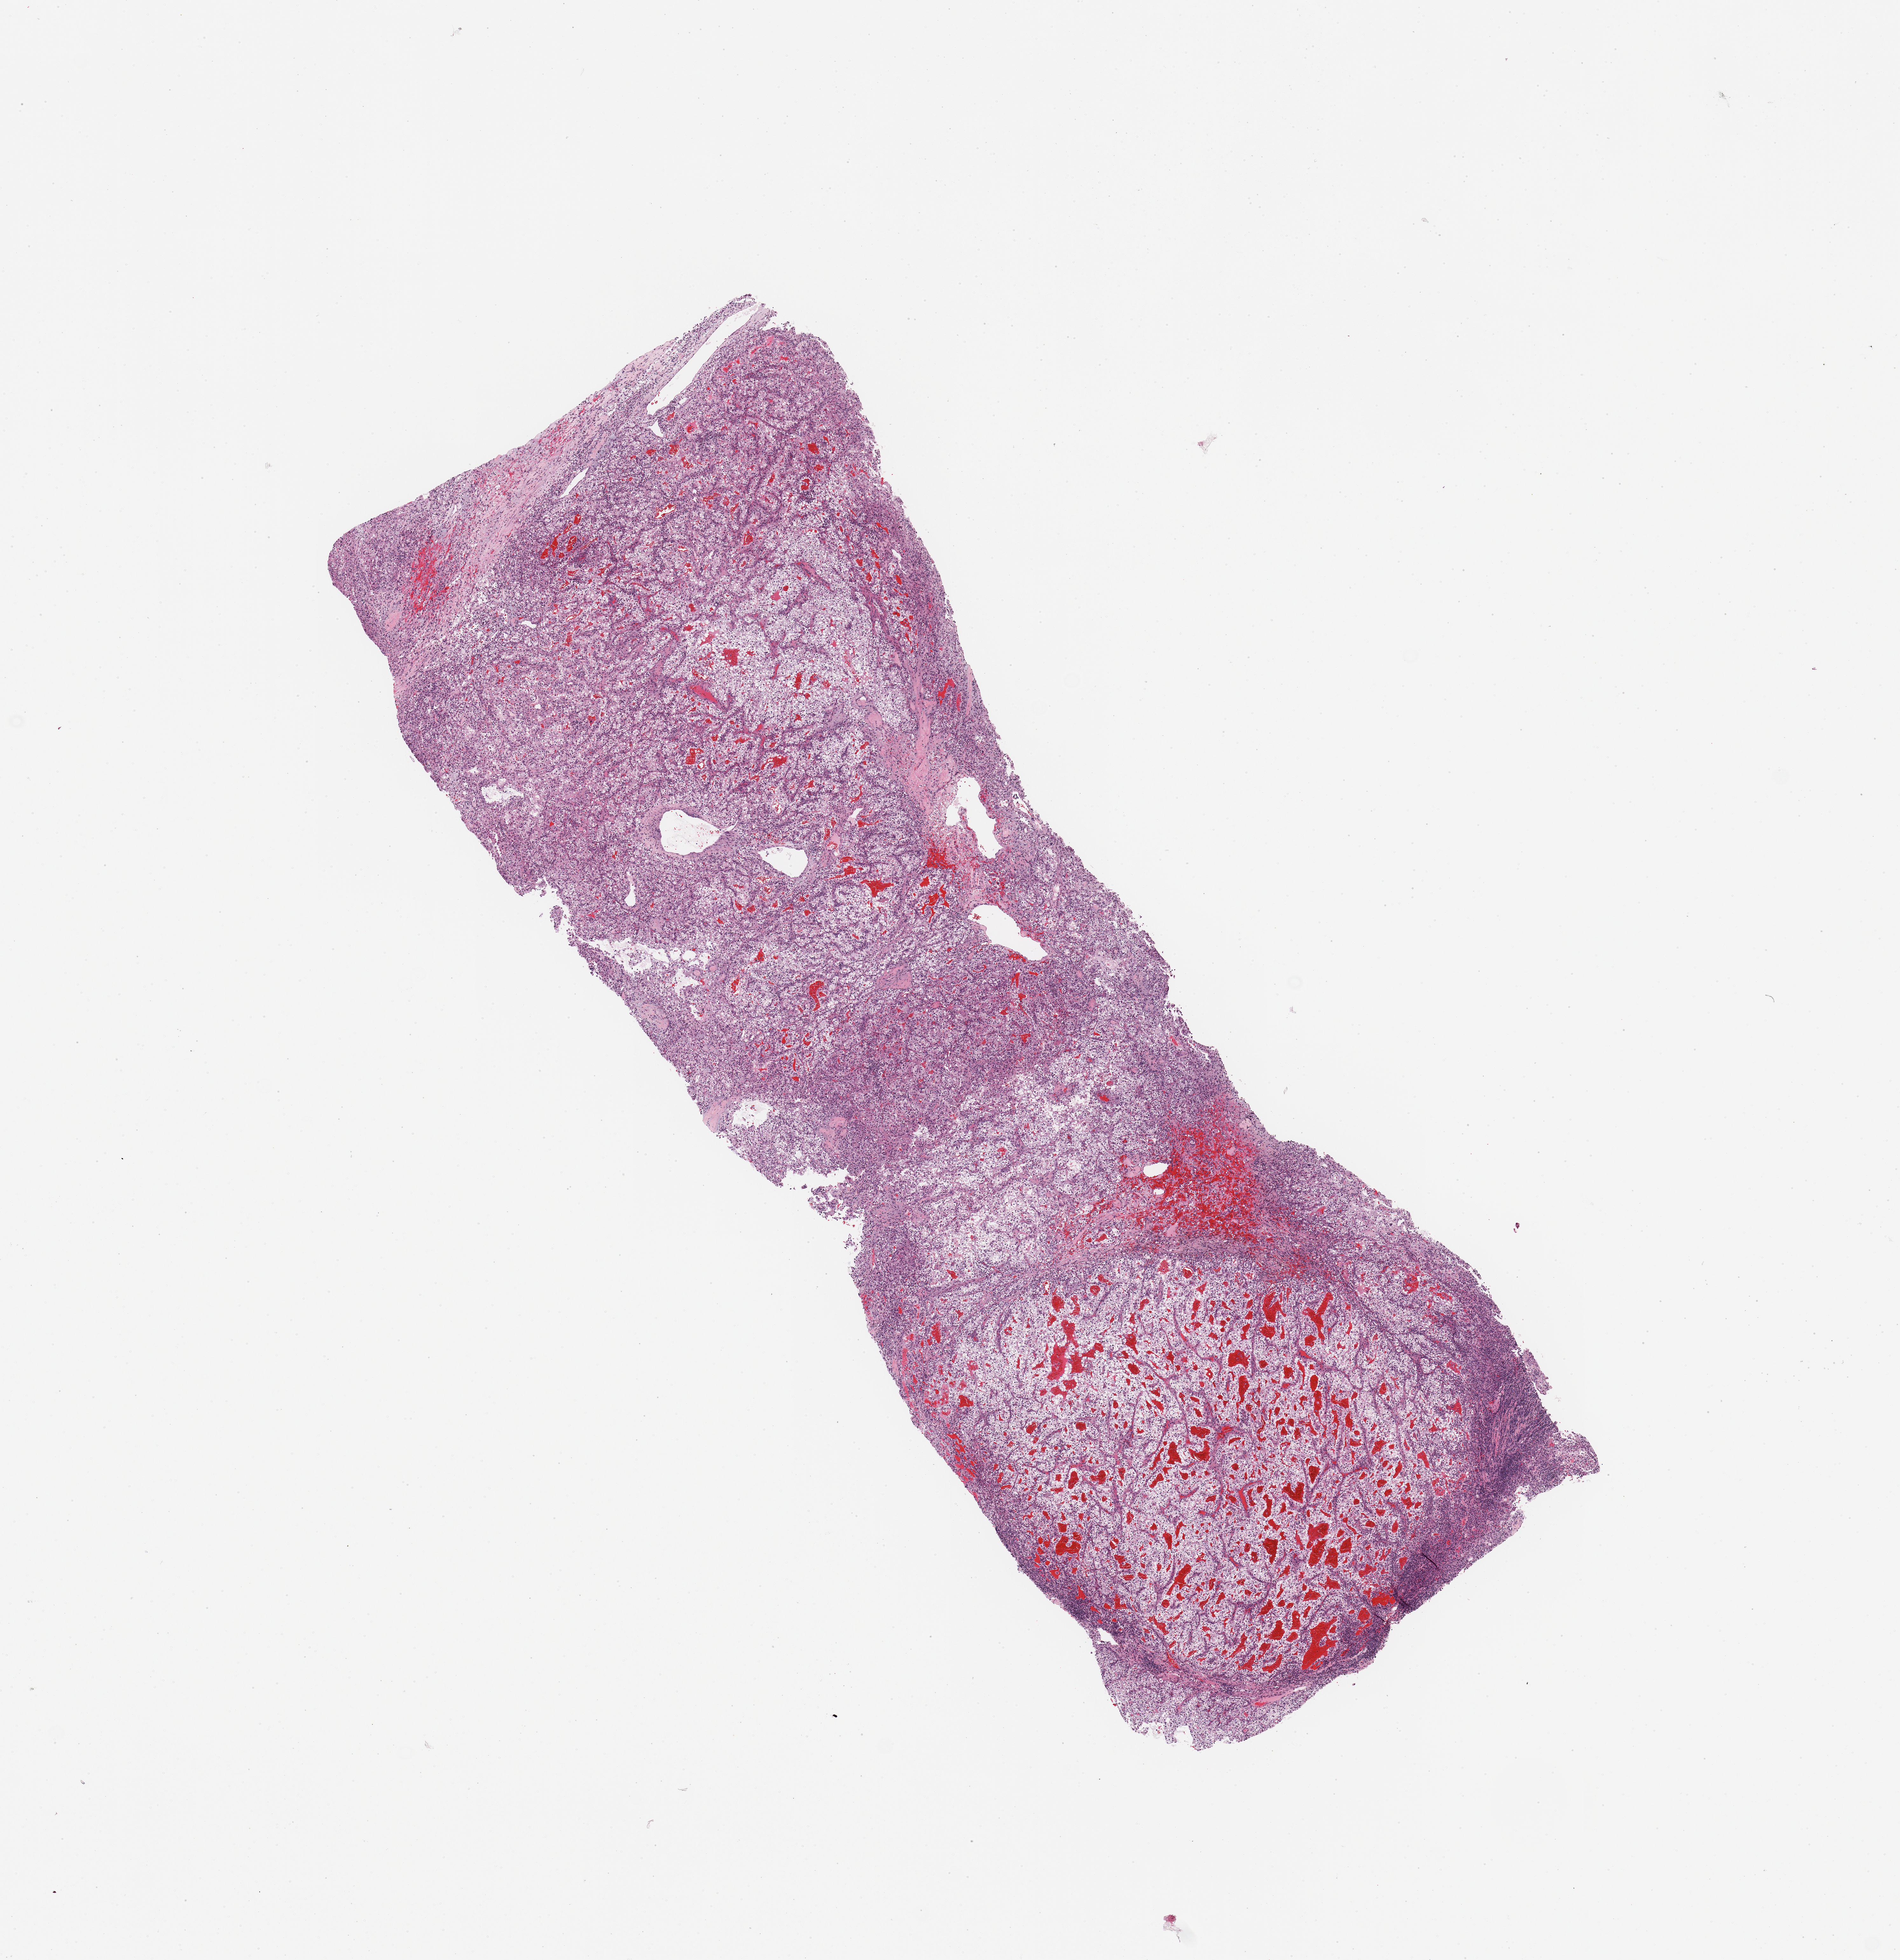
Digitized H&E tissue section (whole slide) — a low-resolution overview of the entire scanned area, about 11.8 x 12.2 mm (slide scanned at 20x); kidney, tumour tissue. Patient: male, age 62 years. Histologic grade: G4 (undifferentiated).
Histologic diagnosis: Renal cell carcinoma, NOS. AJCC pathologic stage: III.